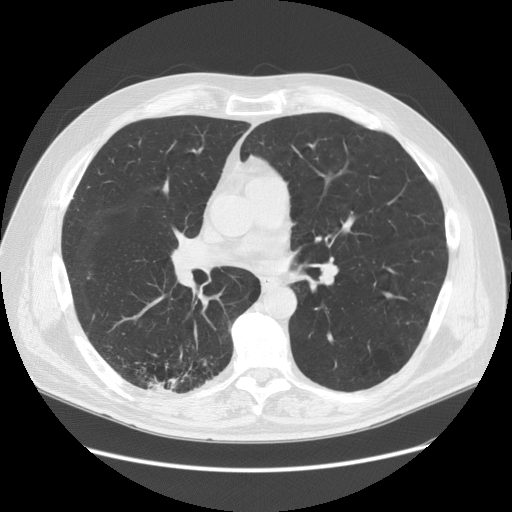
Low-dose screening chest CT, one axial slice. Slice 77 of 149 in the series (ordered by position). Reconstruction kernel STANDARD. Lung window (W 1500 / L -600 HU). 2.5 mm slice thickness. 512 × 512 image matrix.
Structures marked on this image (outlined manually by an expert reader):
- lesion 1 (tumor, lower lobe of right lung): bounding box <147,376,179,391> (left, top, right, bottom; pixels)